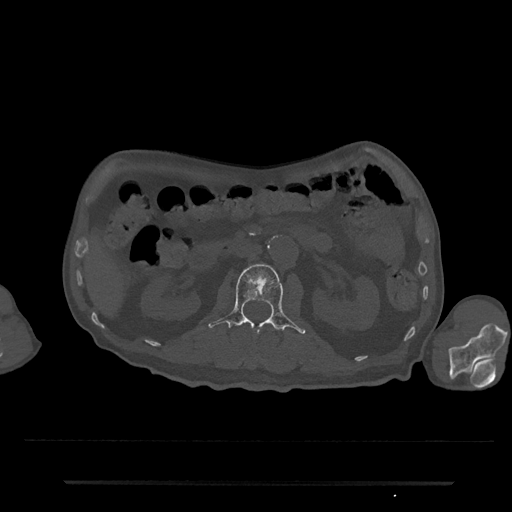
CT including the spine, one axial slice. Slice 72 of 797 in the series (ordered by position). Reconstruction kernel Br40s/3. 120 kVp. Bone window (W 1800 / L 400 HU). 0.5 mm slice thickness. 512 × 512 image matrix, field of view 427 × 427 mm. Patient: male, 74 years. From the clinical record (not read from this slice): primary cancer: prostate.
Annotated regions visible in this slice (semi-automatic segmentation, software-assisted and operator-edited):
- L1 vertebra: bounding box <268,328,271,331> (left, top, right, bottom; pixels)
- L2 vertebra: <208,264,306,334>